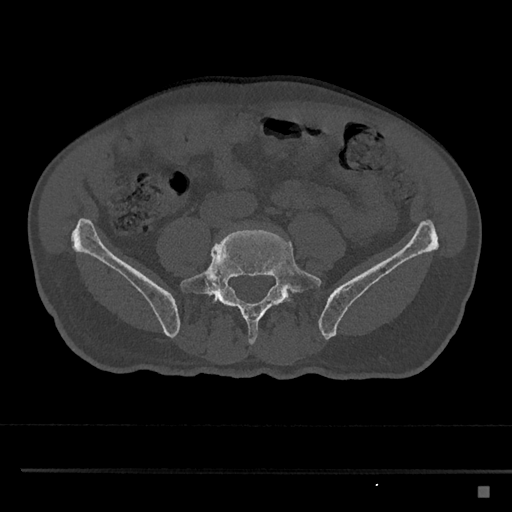
CT including the spine, one axial slice. Position 585 of 797 along the scan axis. Reconstruction kernel Br40s/3. 120 kVp. Bone window (W 1800 / L 400 HU). 512 × 512 image matrix. Male patient, age 59 years. Case-level facts recorded for this patient, not image findings: primary cancer: prostate.
Annotated regions visible in this slice (semi-automatic segmentation, software-assisted and operator-edited):
- L5 vertebra: box from (x=180, y=228) to (x=321, y=345) px